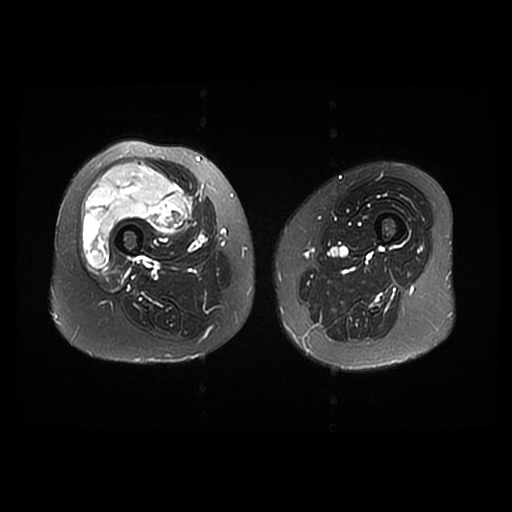
MRI of an extremity soft-tissue mass, one axial slice; position 16 of 42 along the scan axis; T2-weighted fat-saturated; 6 mm slice thickness; 512 × 512 image matrix, field of view 440 × 440 mm. Female patient. Case-level facts recorded for this patient, not image findings: histological type: pleiomorphic undifferentiated sarcoma; grade: high; site of the primary tumour: right quadricep.
Outlined on this slice (manually delineated by an expert):
- gross tumour volume including surrounding oedema: bounding box <81,162,192,269> (left, top, right, bottom; pixels)
- gross tumour volume (mass): <81,162,192,269>